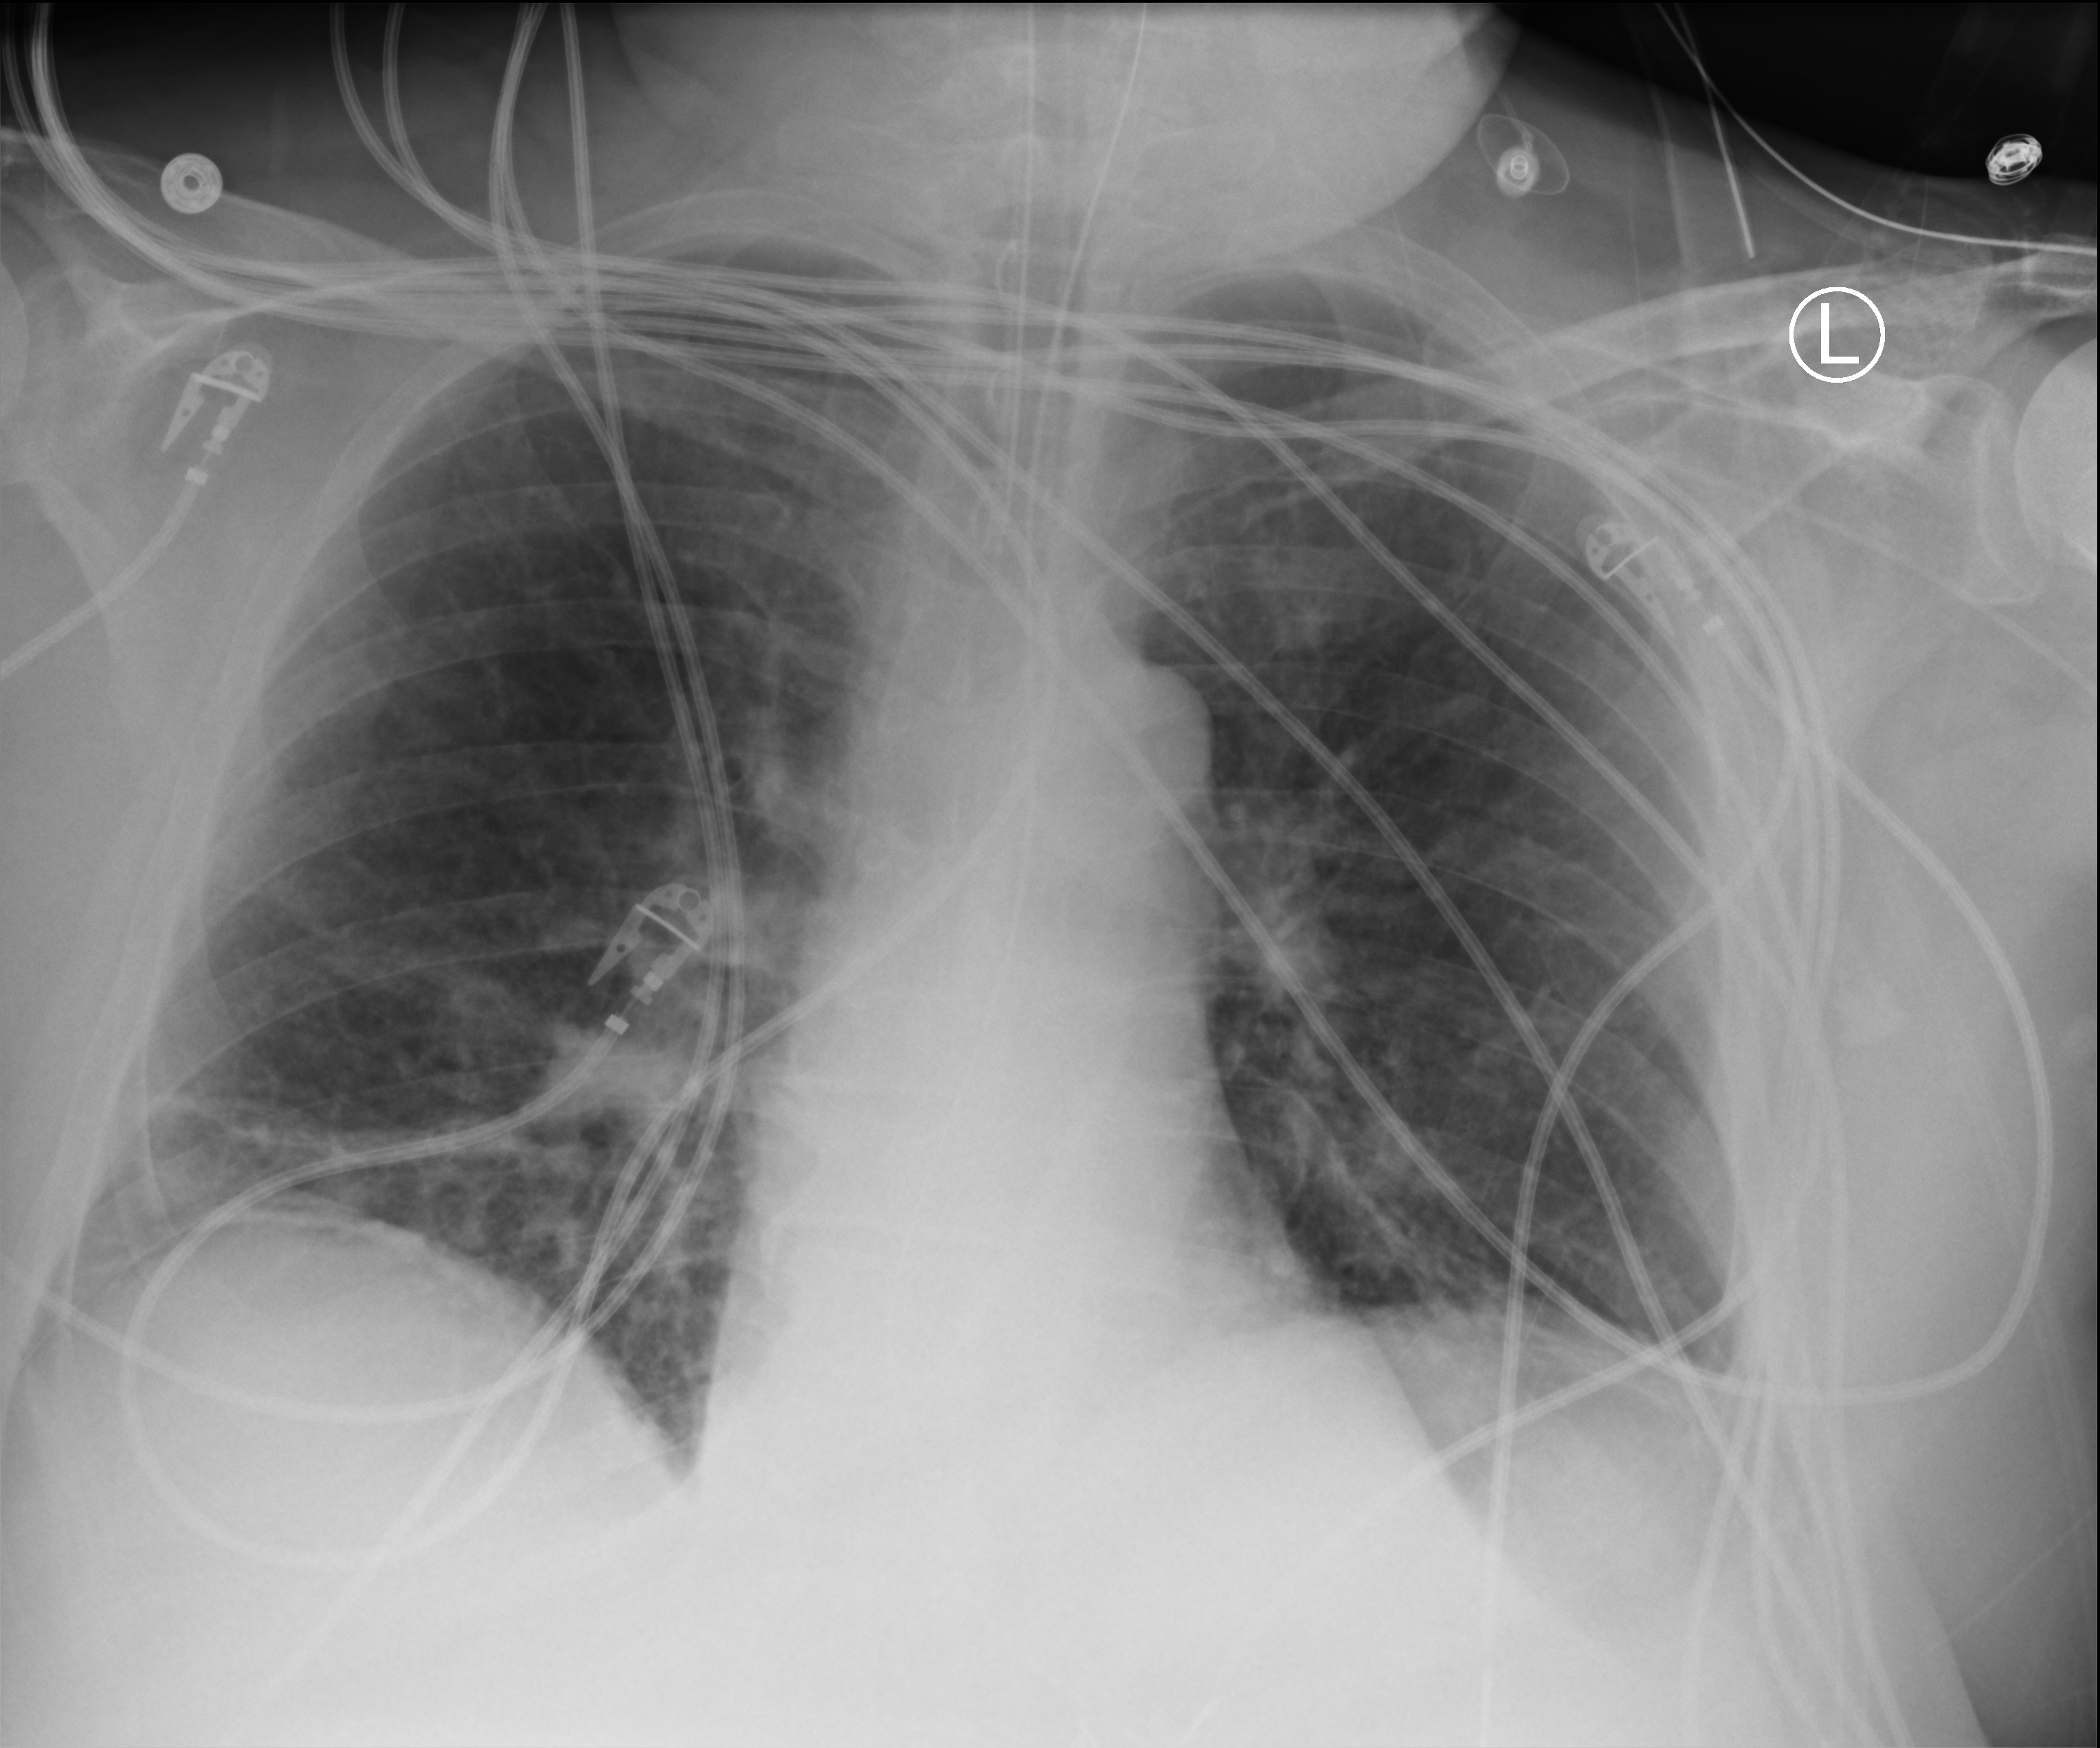
Chest X-ray (portable); anteroposterior (AP) projection. Patient hospitalised with COVID-19; male, aged 60–74 years.
Admission-level facts for this patient (not findings on this image; timing relative to this image not recorded):
- admitted to intensive care during this hospital stay: yes